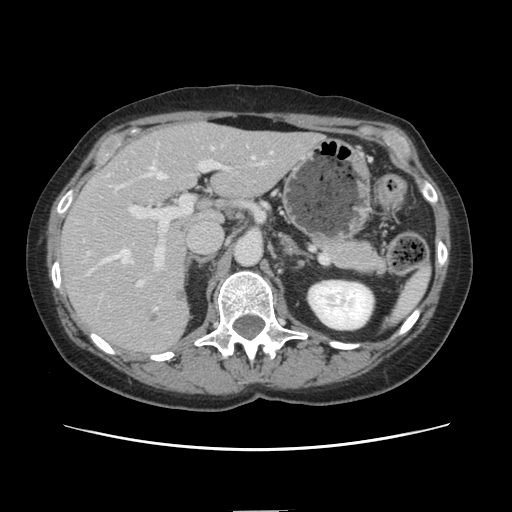
Contrast-enhanced abdominal CT, one axial slice; position 81 of 141 along the scan axis; 120 kVp; intravenous contrast given; soft-tissue window (W 400 / L 40 HU); 512 × 512 image matrix, field of view 350 × 350 mm. Female patient, age 63 years. Case-level facts recorded for this patient, not image findings: diagnosis: colorectal cancer liver metastases, imaged before liver resection; multiple liver metastases: yes; largest metastasis: 3.2 cm; disease in both lobes: yes.
Annotated regions visible in this slice (expert manual segmentation):
- hepatic veins: bounding box <85,157,254,277> (left, top, right, bottom; pixels)
- liver: <60,123,319,354>
- planned liver remnant (the part of the liver to remain after resection): <175,123,319,222>
- portal vein (with intrahepatic branches): <129,150,259,289>
- liver metastasis: <173,289,187,303>
- liver metastasis: <147,314,160,324>